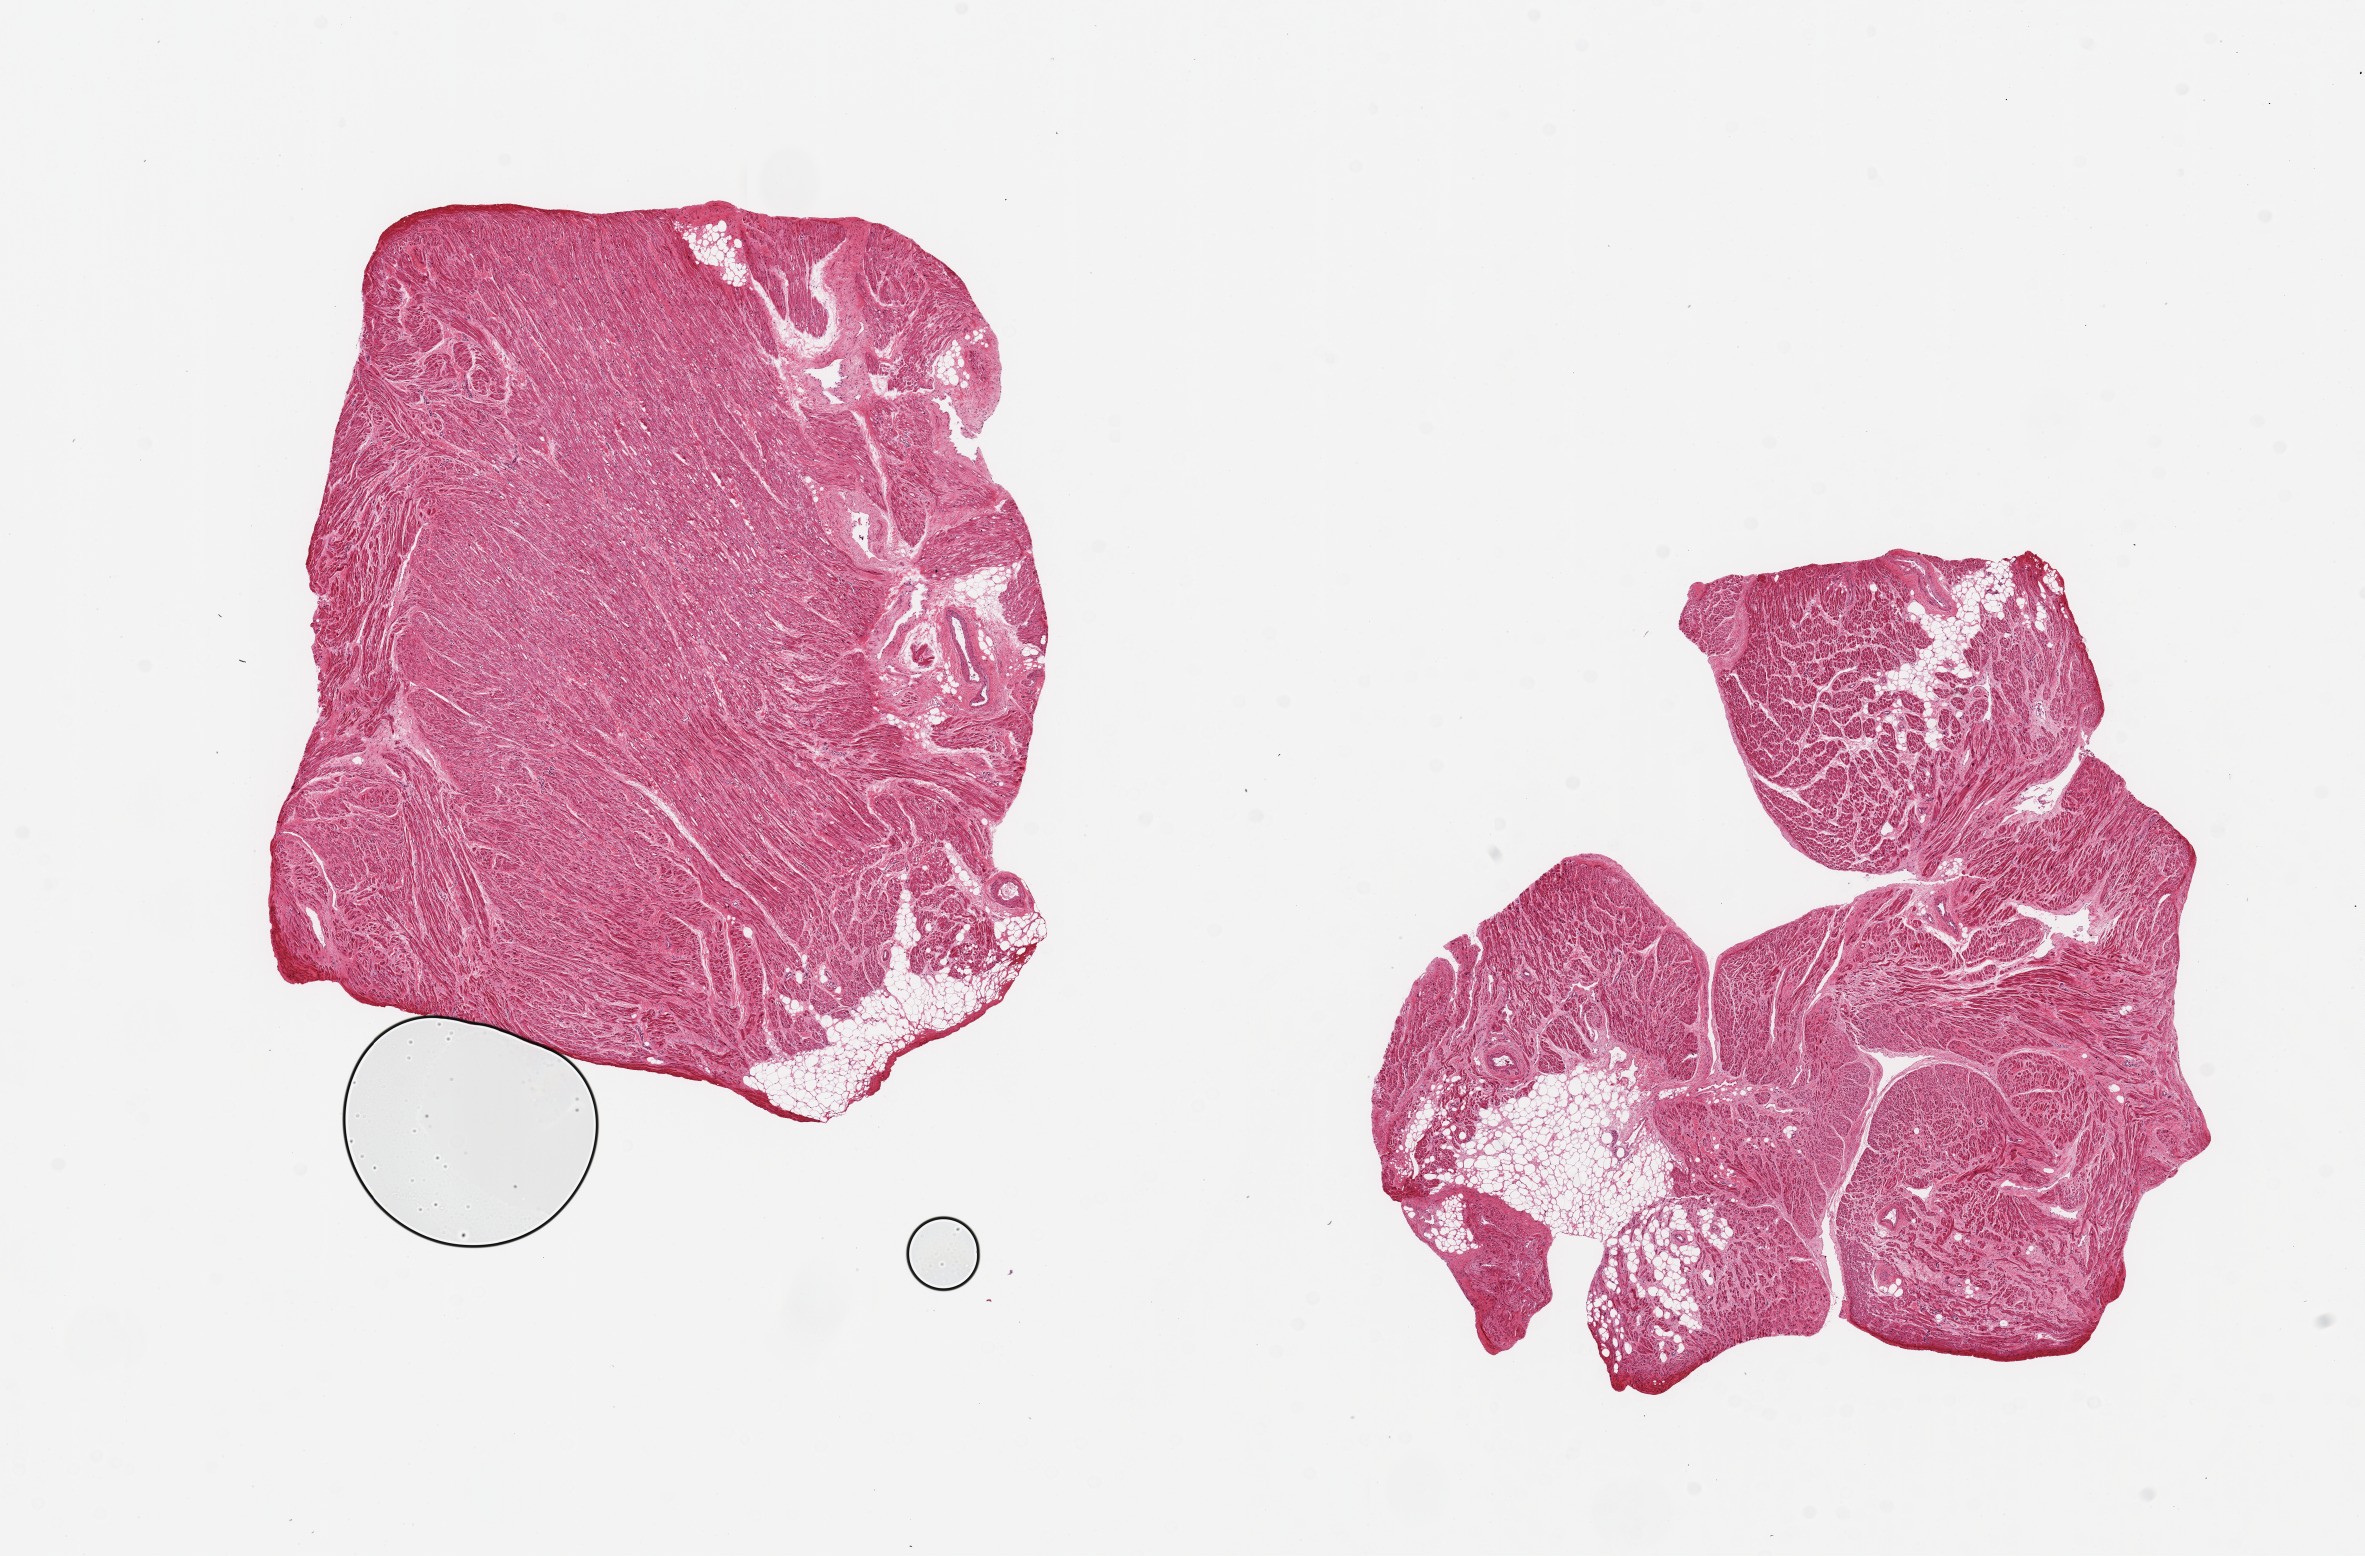
Whole-slide image, haematoxylin and eosin stain, a low-resolution overview of the entire scanned area, about 18.7 x 12.3 mm. PAXgene-fixed paraffin-embedded (PFPE) section. Target tissue: auricular appendage. Tissue donor sample. Donor sex: male.
- pathologist's review note for this sample: 2 pieces ?atrial appendage? ~6x6mm